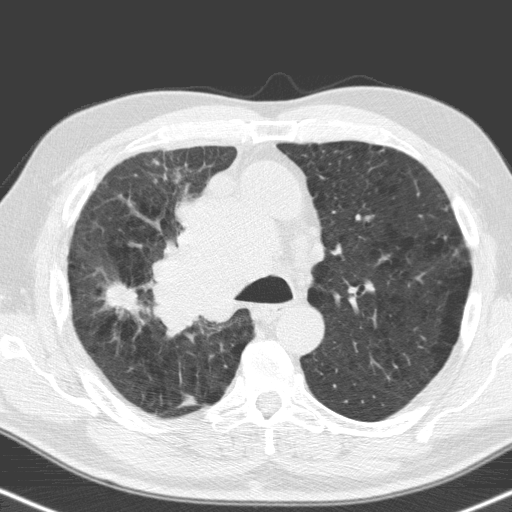
Axial slice from a low-dose chest CT screening exam, baseline annual screen, lung window (W 1500 / L -600 HU), 120 kVp, slice 49 of 160 in the series. Male participant, aged 71 years at enrolment.
Lesion marked by an expert reader, bounding box [x1, y1, x2, y2] px = [88, 271, 161, 338]. The screening reader recorded 2 non-calcified nodules or masses ≥4 mm on this exam (right upper lobe, right upper lobe); which of them this box marks is not recorded. Lung cancer was diagnosed 31 days after this screen: small cell carcinoma, NOS, right upper lobe, stage IV (AJCC 6th edition), 40 mm at pathology.